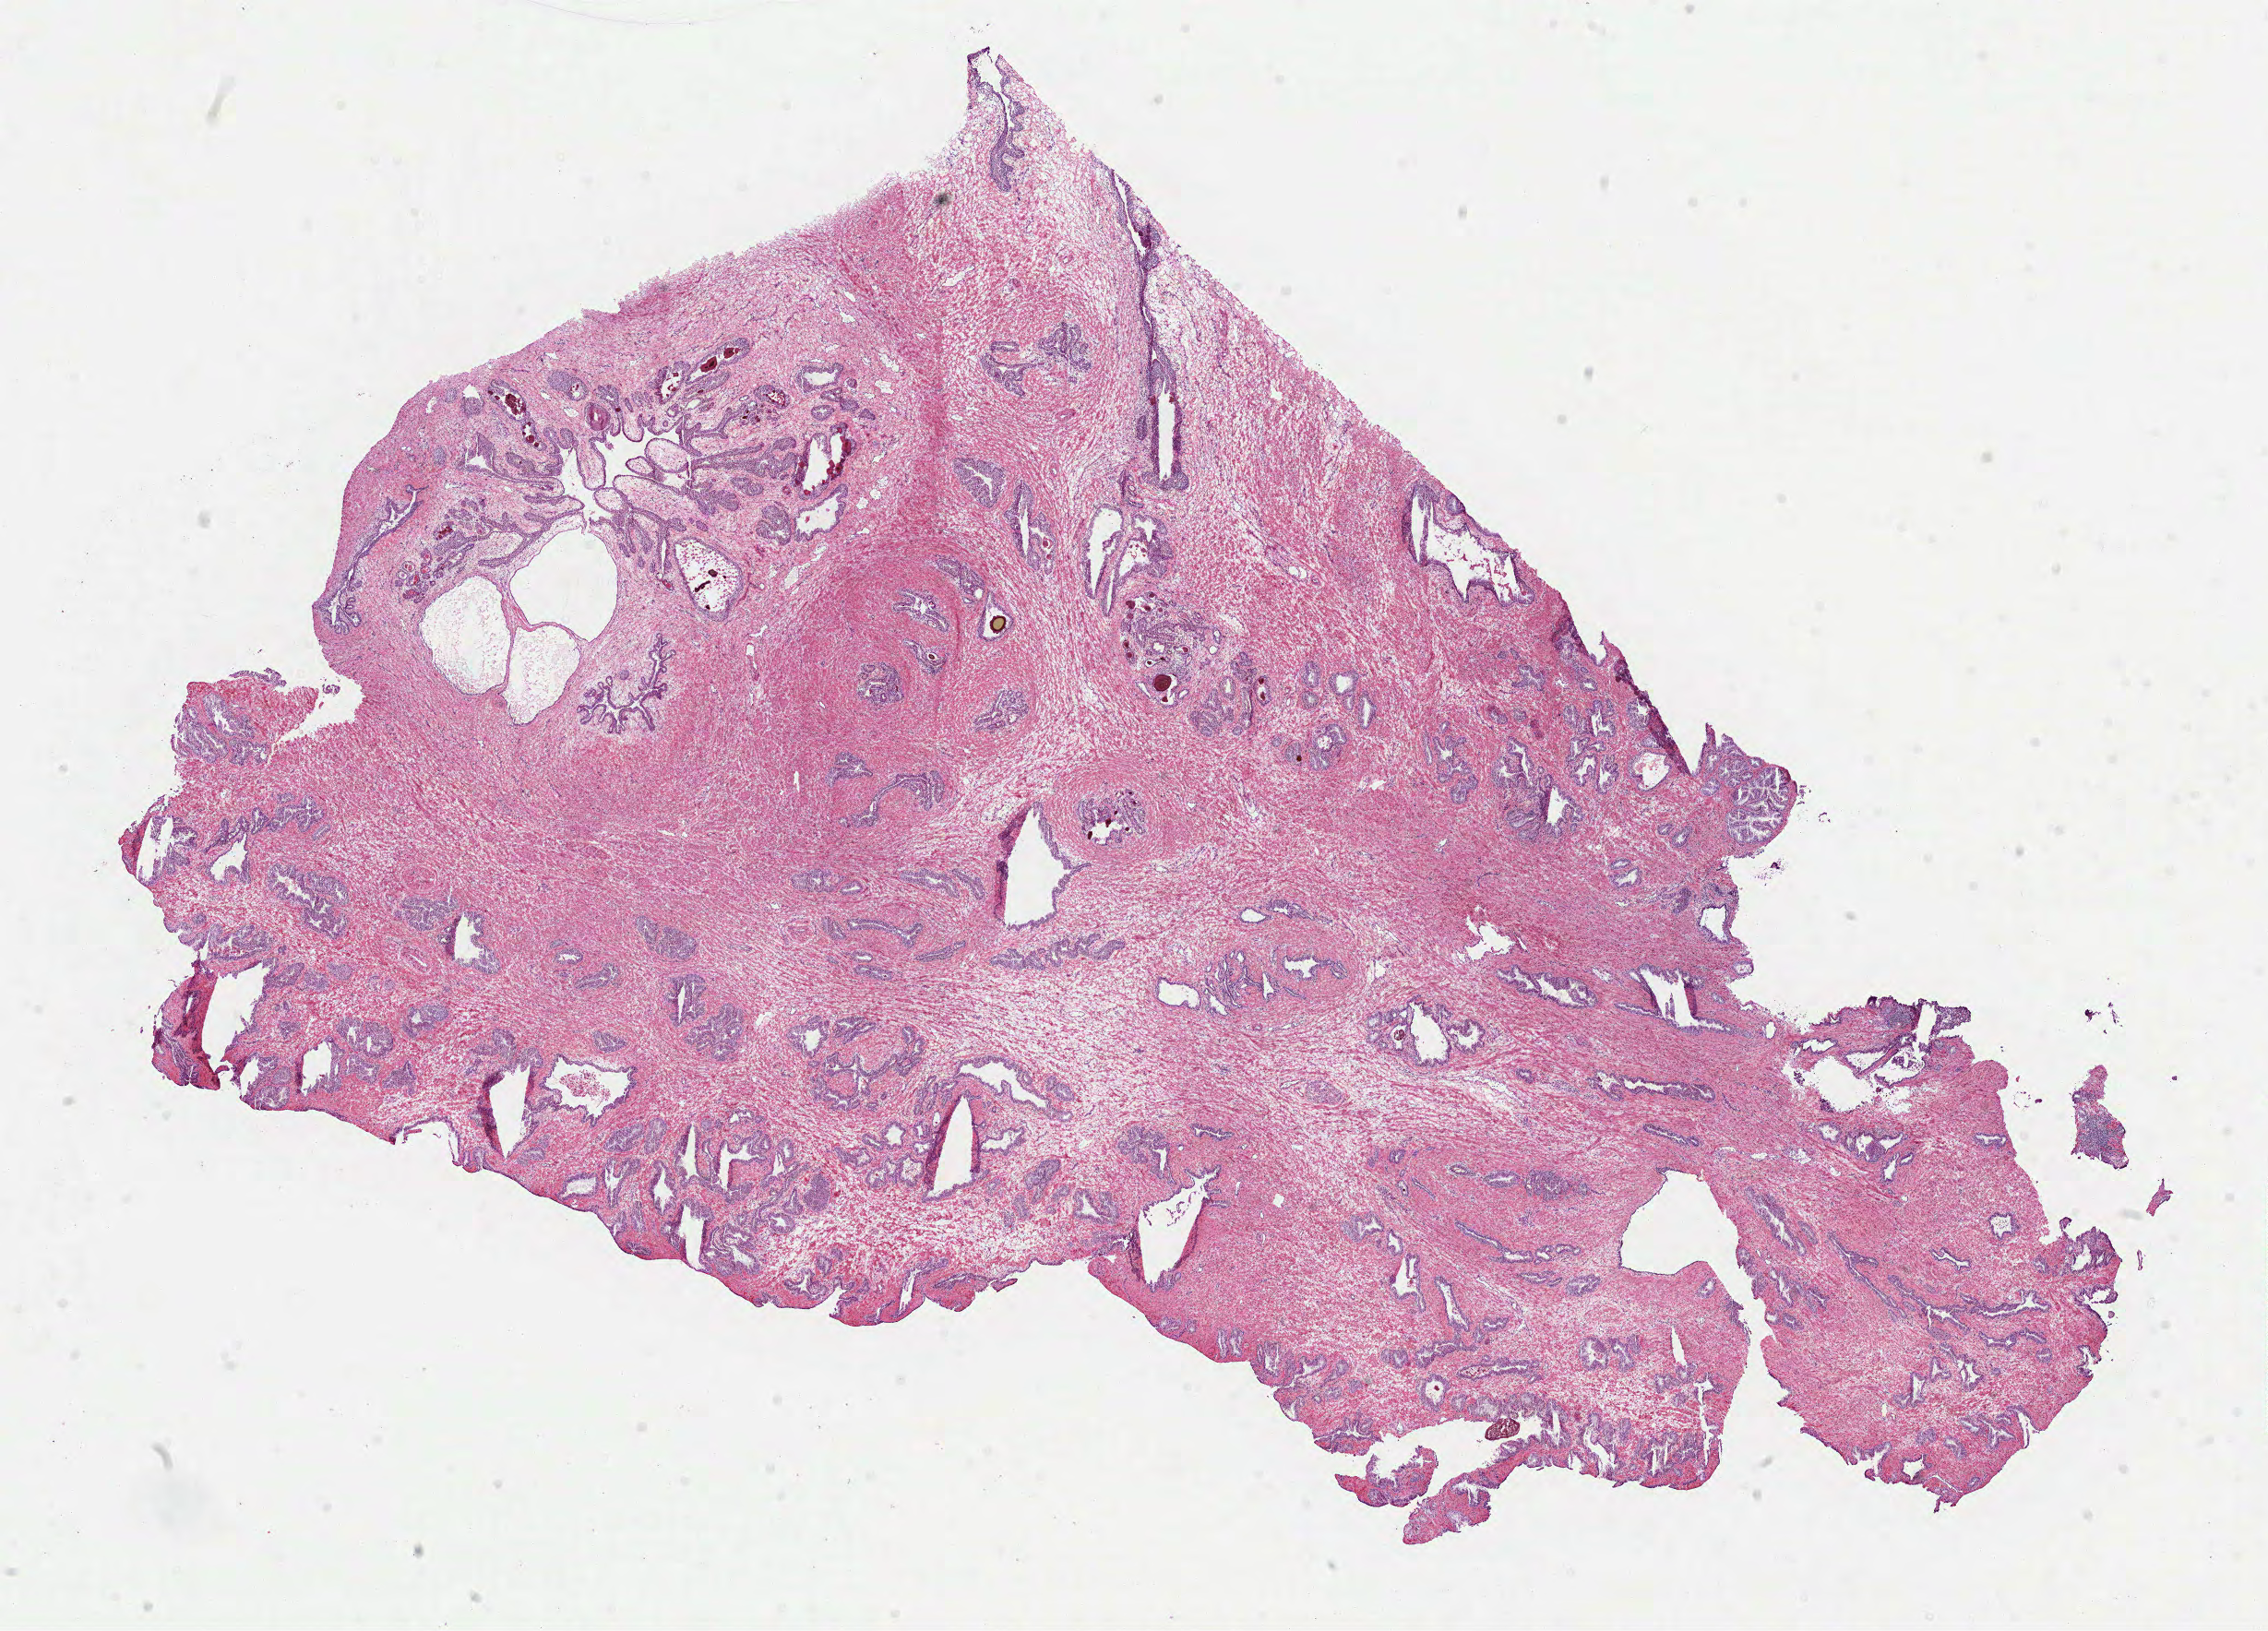
Digitized H&E tissue section (whole slide), shown as a low-resolution overview of the whole scanned area (about 19.8 x 14.3 mm, from a 40x scan). Frozen section from the top of the tissue portion. Prostate, solid tissue normal (non-tumour tissue) sample. Male patient; age at initial diagnosis 66 years.
This section: solid tissue normal sample (biorepository sample class). Patient diagnosis: Acinar cell carcinoma (prostate gland).